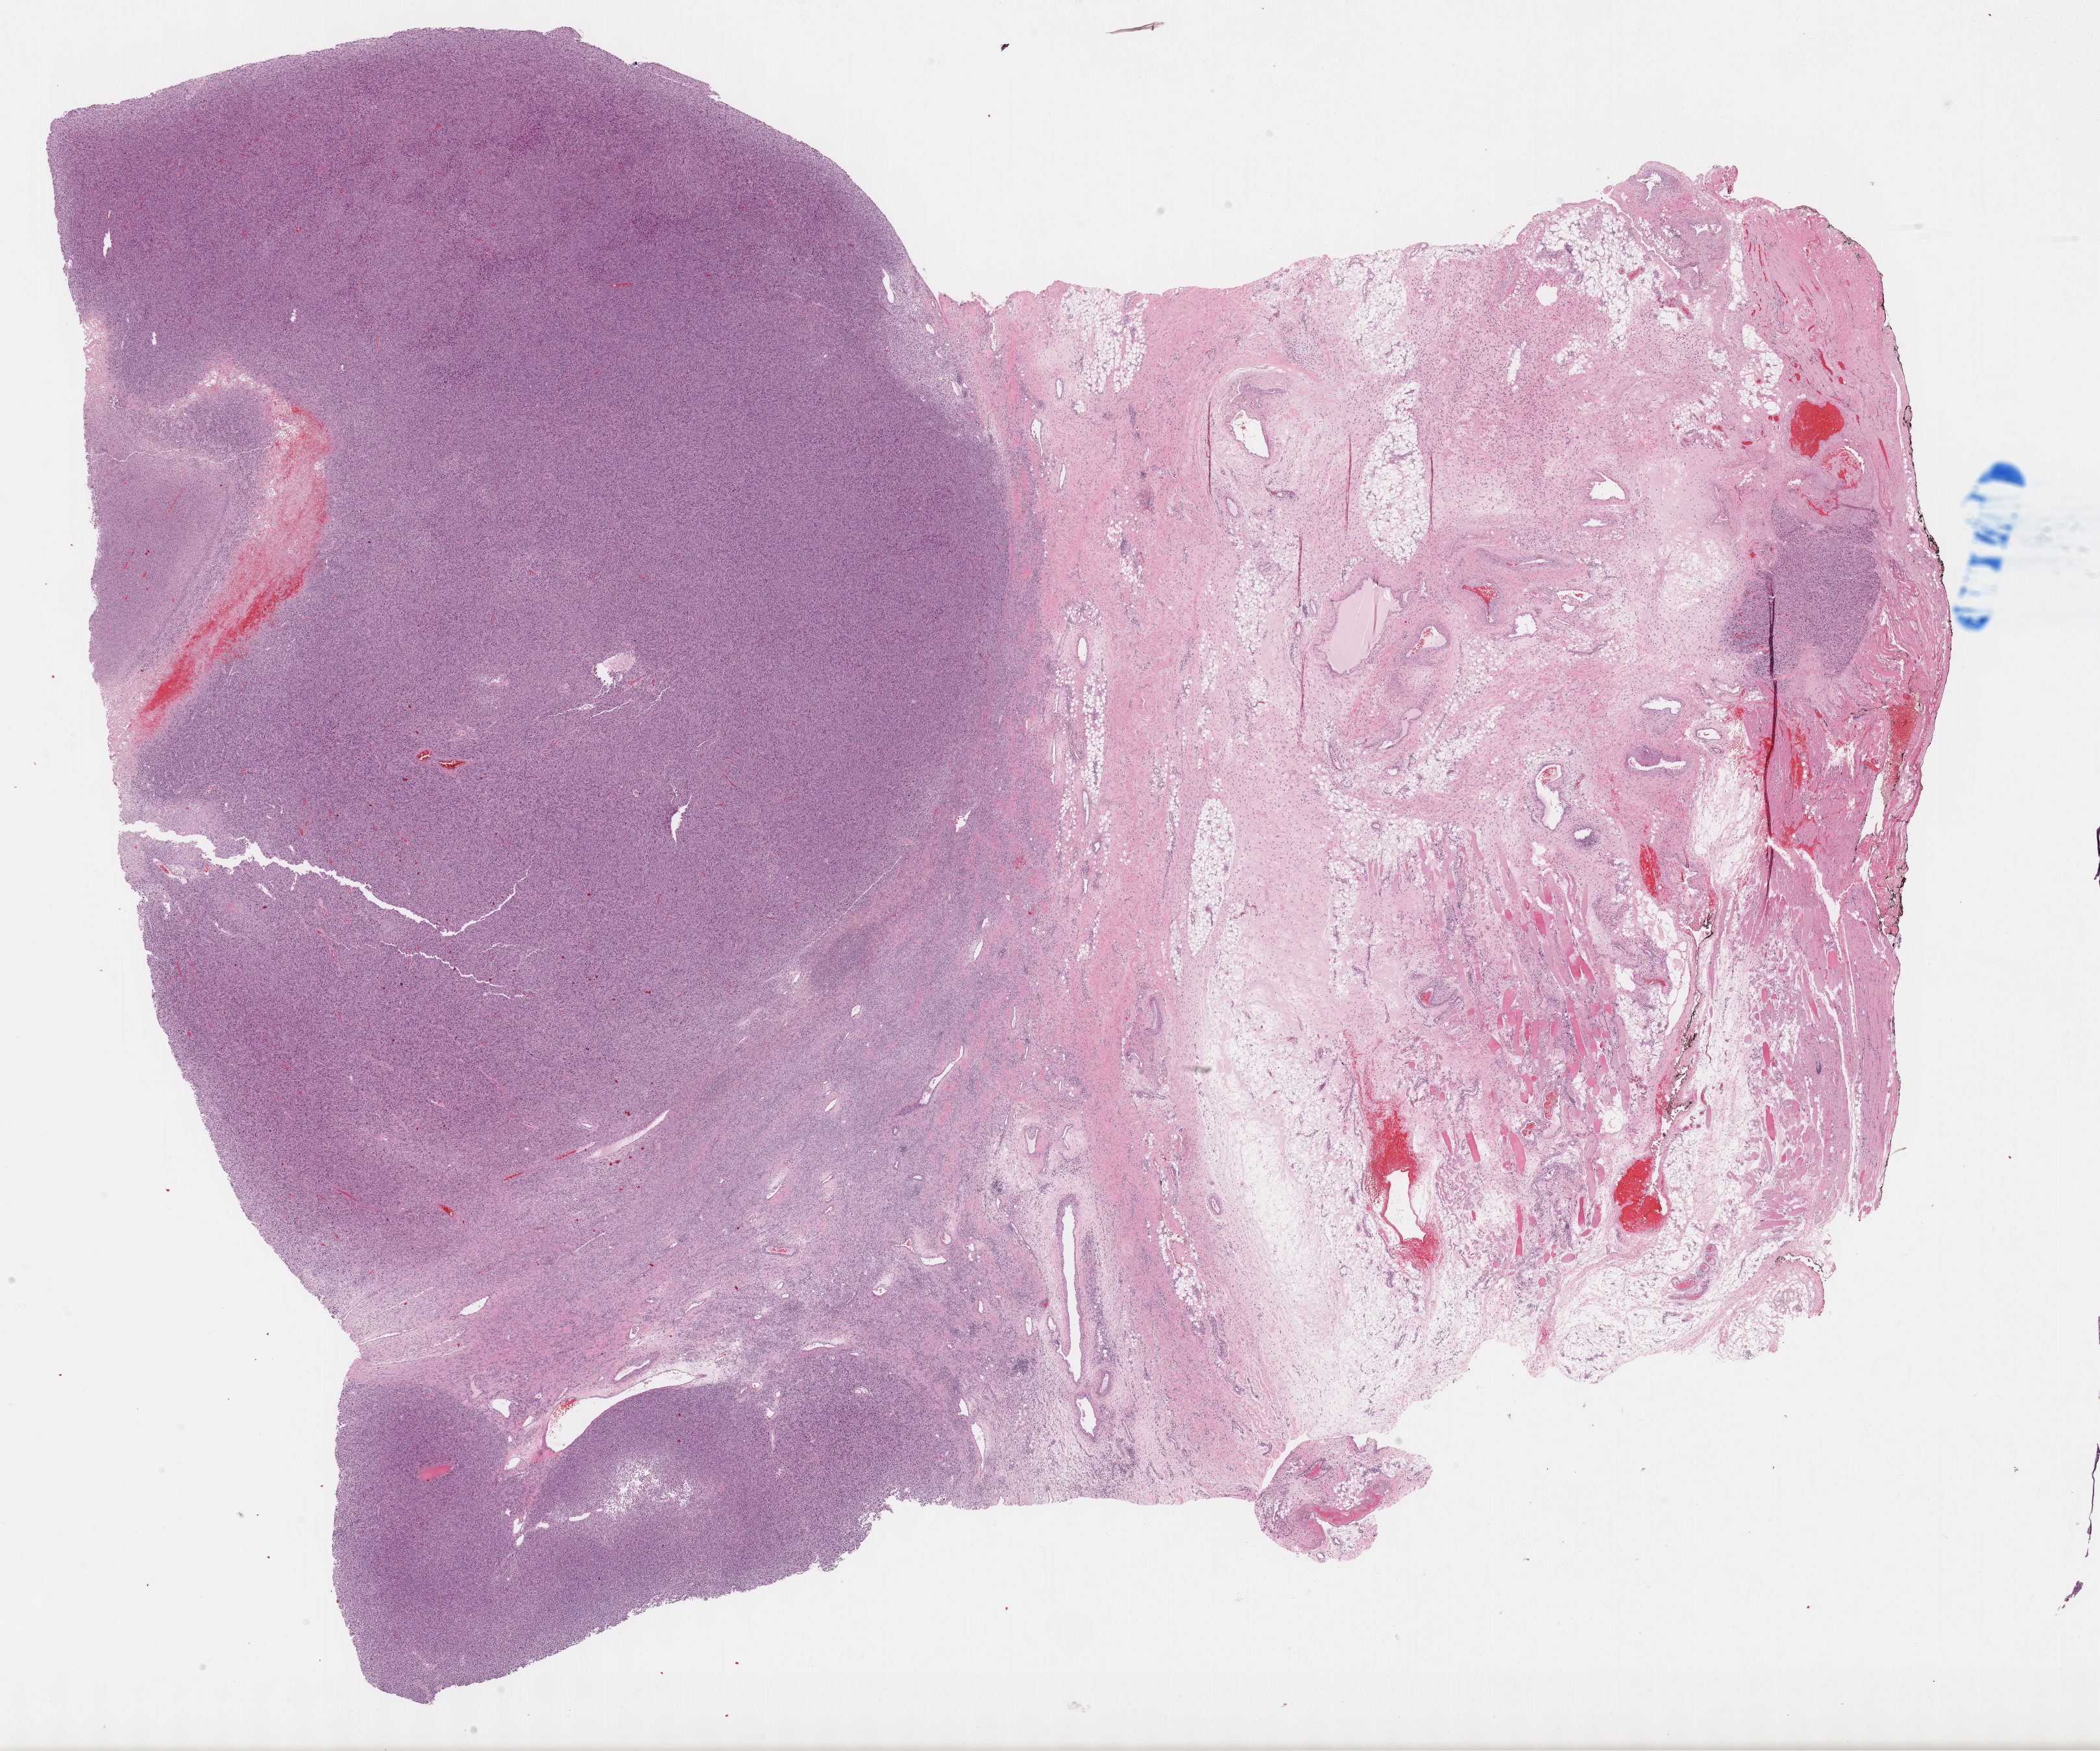
Whole-slide histology image, Hematoxylin and eosin (H&E) stained, a low-resolution overview of the entire scanned area, about 26.2 x 21.8 mm (from a 40x scan). FFPE section. Sample: primary tumour, connective, subcutaneous and other soft tissues. Female, age 78 years at initial diagnosis.
Pathologic diagnosis: Leiomyosarcoma, NOS (connective, subcutaneous and other soft tissues of pelvis).